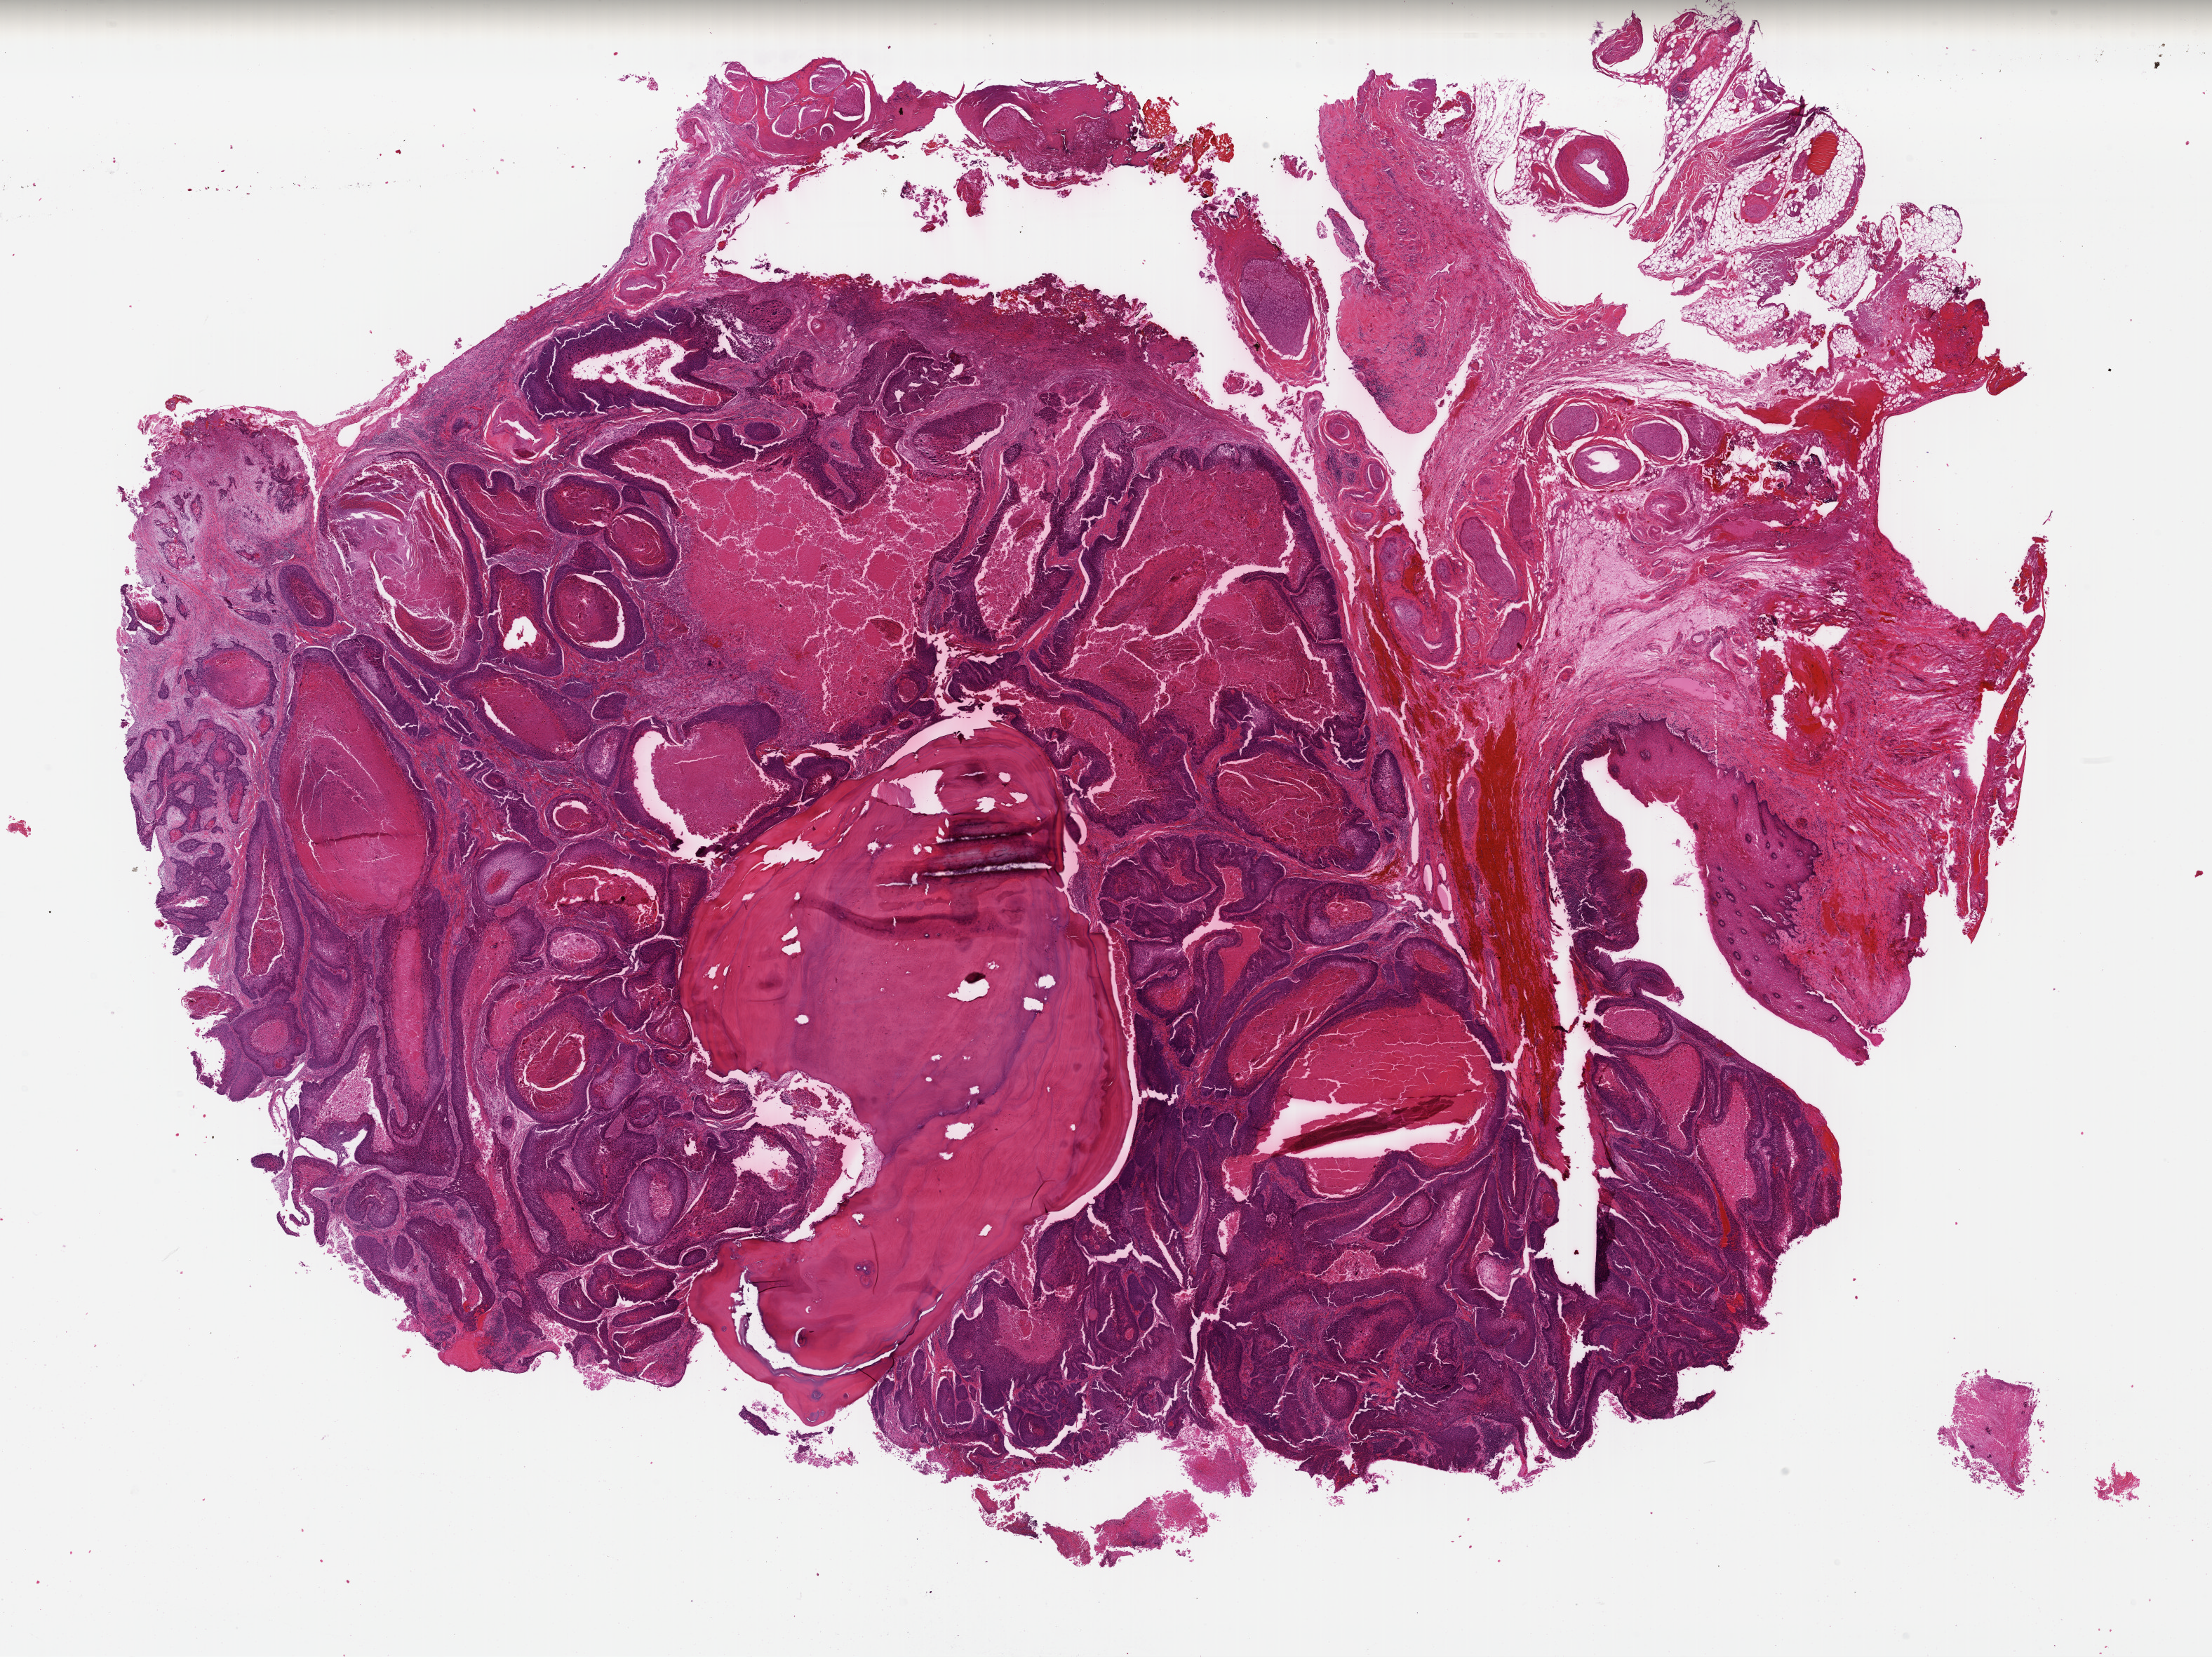
Digitized Hematoxylin and eosin (H&E) stained tissue section (whole slide) — a low-resolution overview of the entire scanned area, about 24.8 x 18.6 mm (acquisition: 40x scan). Formalin-fixed paraffin-embedded (FFPE) diagnostic section. Head and neck, primary tumour sample. Male patient; age at initial diagnosis 84 years. Histologic grade: G2 (moderately differentiated).
- lymph nodes positive (case pathology): 1 of 16 examined
- pathologic diagnosis: Squamous cell carcinoma, NOS
- AJCC pathologic stage: III (7th edition)
- laterality: right